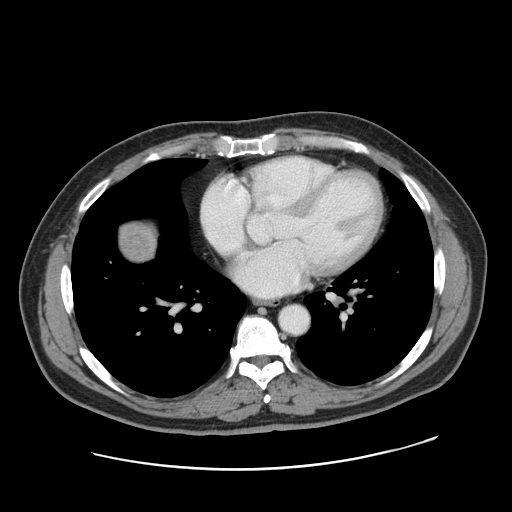
Contrast-enhanced abdominal CT, one axial slice; slice 169 of 178 in the series (ordered by position); soft-tissue window (W 400 / L 40 HU); 2.5 mm slice thickness; 512 × 512 image matrix. Male patient, age 63 years. Case-level facts recorded for this patient, not image findings: diagnosis: colorectal cancer liver metastases, imaged before liver resection; multiple liver metastases: yes; largest metastasis: 8 cm; disease in both lobes: yes.
Annotated regions visible in this slice (manually delineated by an expert):
- liver: box from (x=120, y=223) to (x=156, y=260) px
- liver metastasis: (x=123, y=227)–(x=158, y=260)